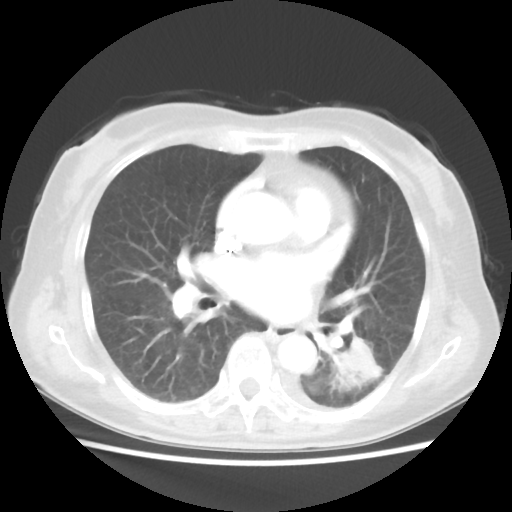
Chest CT, one axial slice; position 18 of 40 along the scan axis; reconstruction kernel STANDARD; lung window (W 1500 / L -600 HU); 5 mm slice thickness; 512 × 512 image matrix, field of view 341 × 341 mm. Female patient, age 69 years. Case-level facts recorded for this patient, not image findings: clinical TNM (as recorded): T1c N0 M0.
Structures marked on this image (rectangle marked by the reading radiologist):
- lung tumour (recorded histology: adenocarcinoma): box from (x=328, y=328) to (x=383, y=392) px